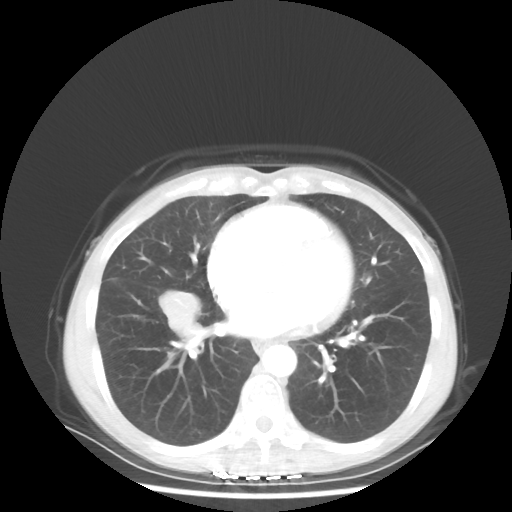
Chest CT, one axial slice; position 23 of 56 along the scan axis; lung window (W 1500 / L -600 HU); 5 mm slice thickness; 512 × 512 image matrix, field of view 360 × 360 mm. Patient: female, 57 years. From the clinical record (not read from this slice): clinical TNM (as recorded): T1c N3 M1a; histopathological grade: G3.
Structures marked on this image (rectangle marked by the reading radiologist):
- lung tumour (recorded histology: adenocarcinoma): bounding box (x1, y1, x2, y2) in pixels: (157, 288, 199, 338)